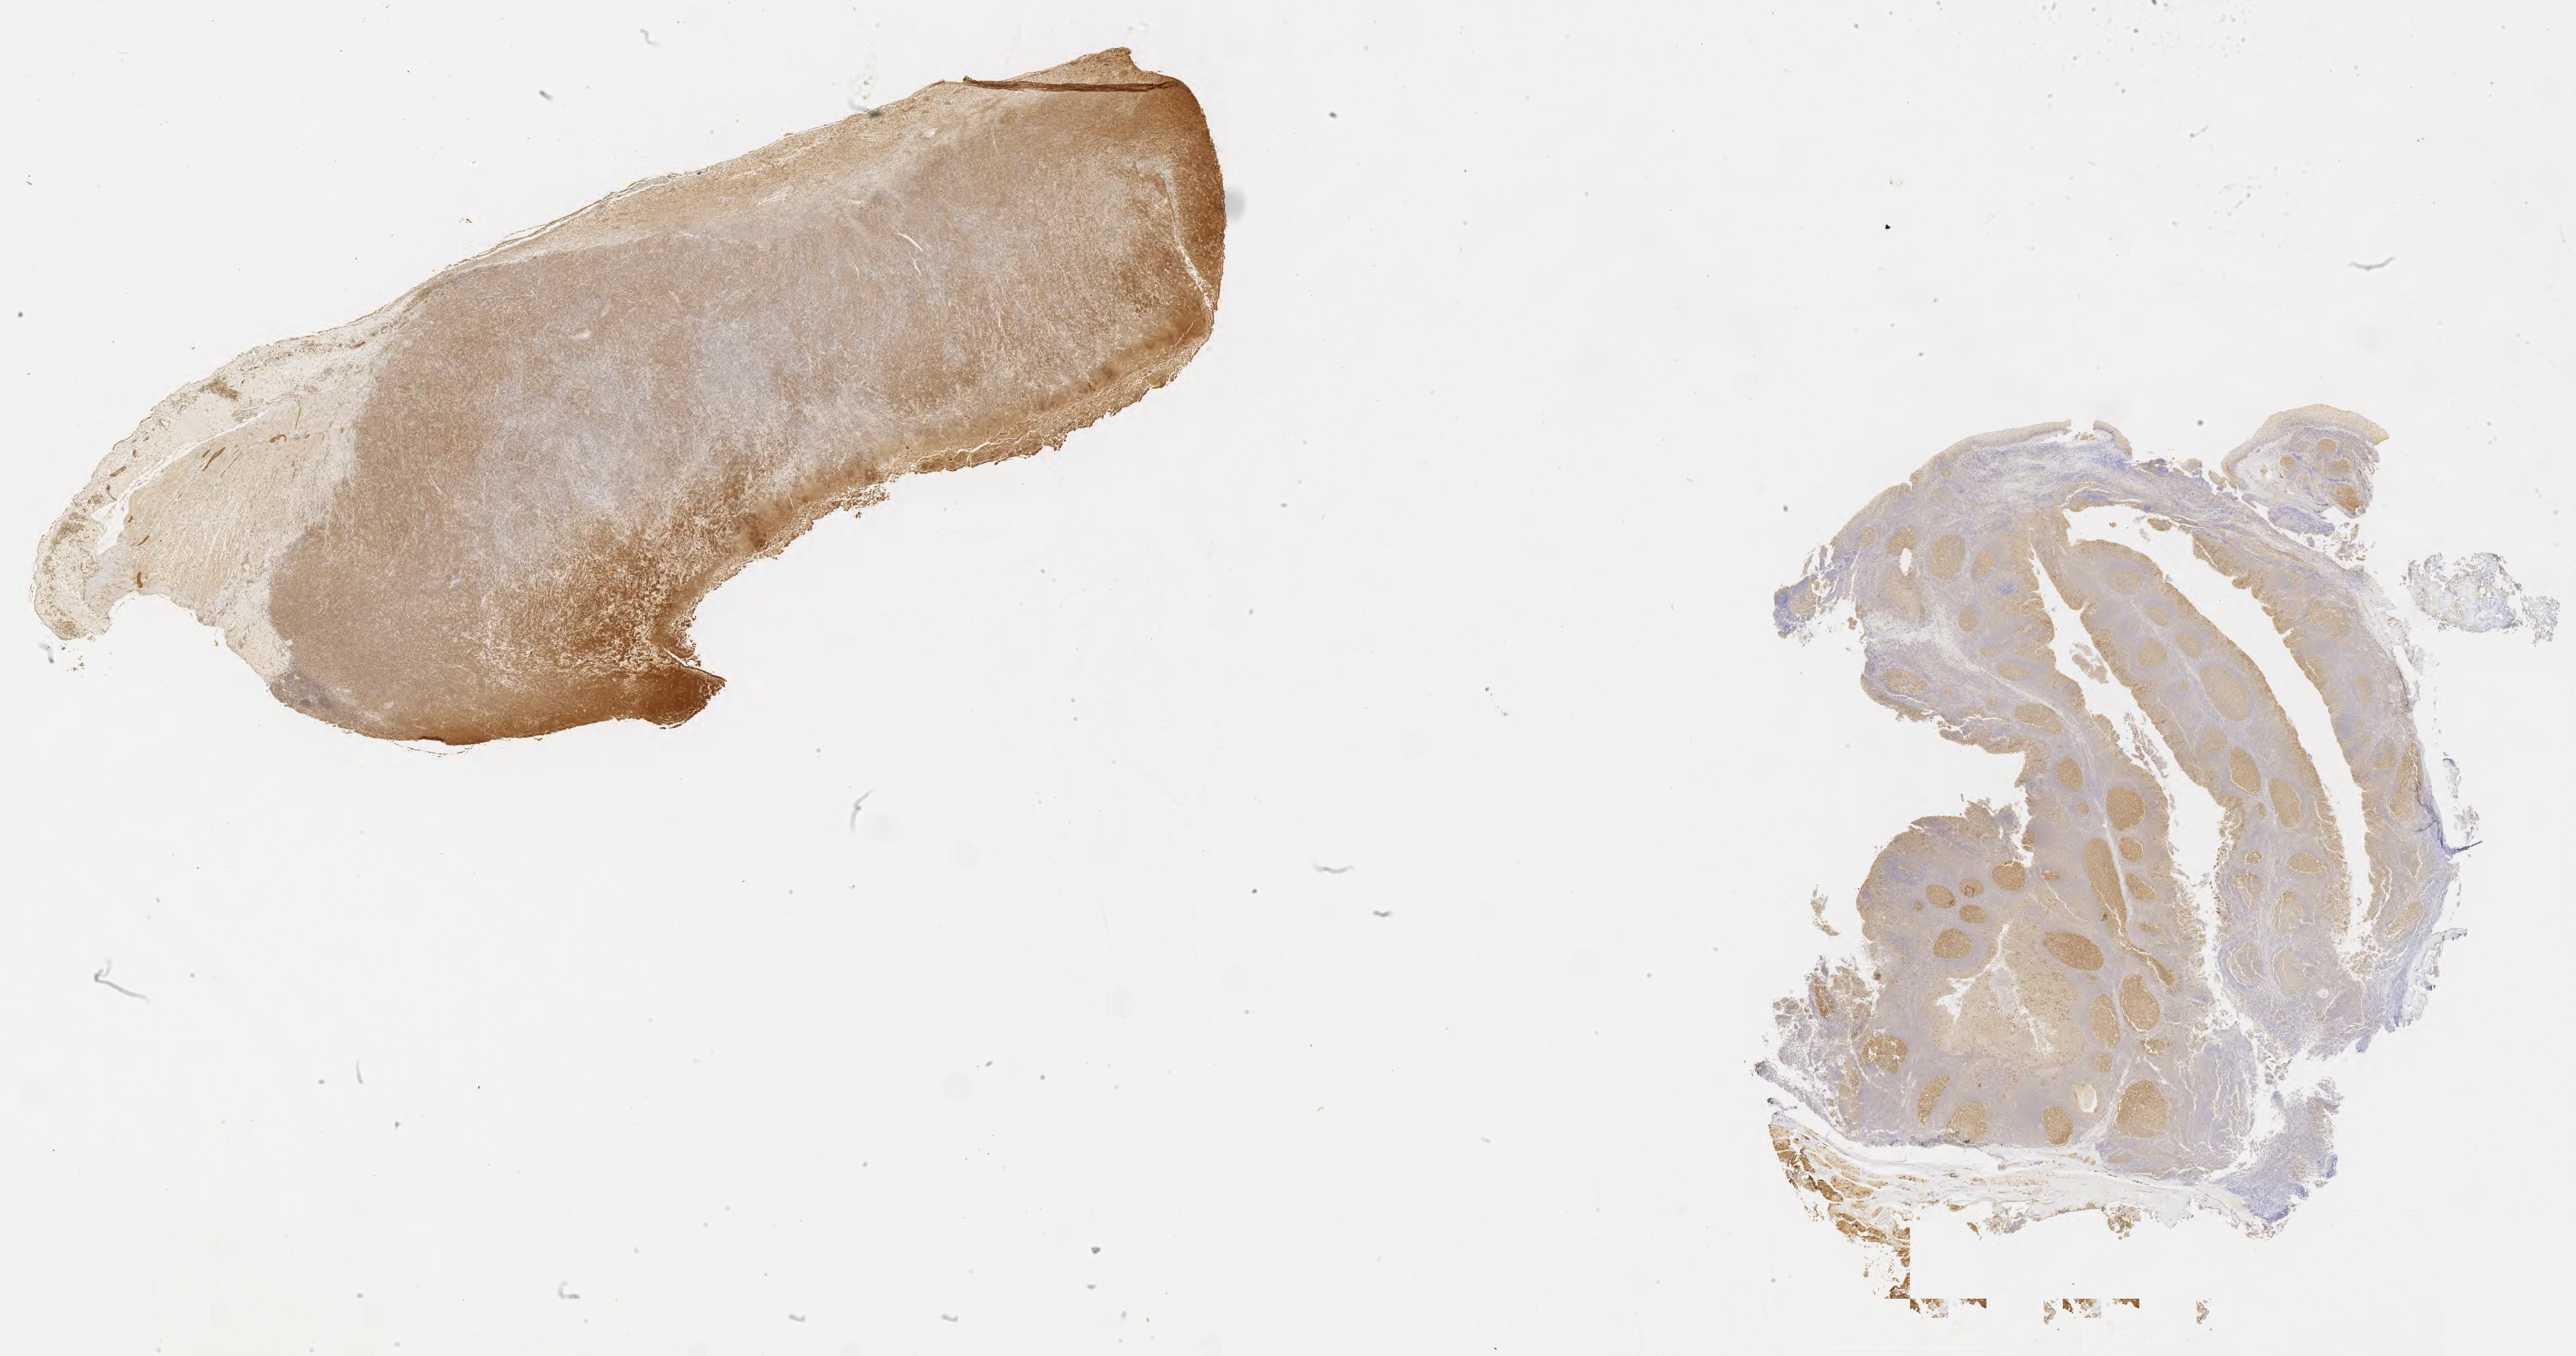
IHC for BCL6, whole-slide image — low-resolution overview of the scanned area, about 32.7 x 17.2 mm; tumor tissue; site: small intestine. Male, age 3 years at initial diagnosis.
Diagnosis: Burkitt lymphoma, NOS.